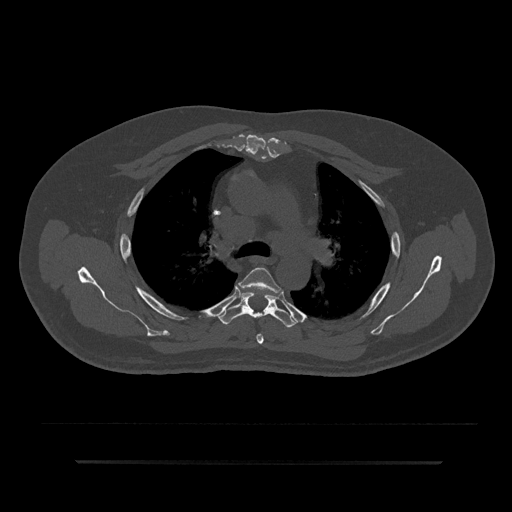
CT including the spine, one axial slice. Position 592 of 797 along the scan axis. Reconstruction kernel Br40s/3. 120 kVp. Bone window (W 1800 / L 400 HU). 0.5 mm slice thickness. 512 × 512 image matrix. Patient: male, 59 years. Case-level facts recorded for this patient, not image findings: primary cancer: bile ducts; vertebrae with lytic lesions (as recorded): T10.
Outlined on this slice (semi-automatically segmented with operator editing):
- T4 vertebra: bounding box (x1, y1, x2, y2) in pixels: (238, 267, 281, 344)
- T5 vertebra: (218, 292, 298, 327)